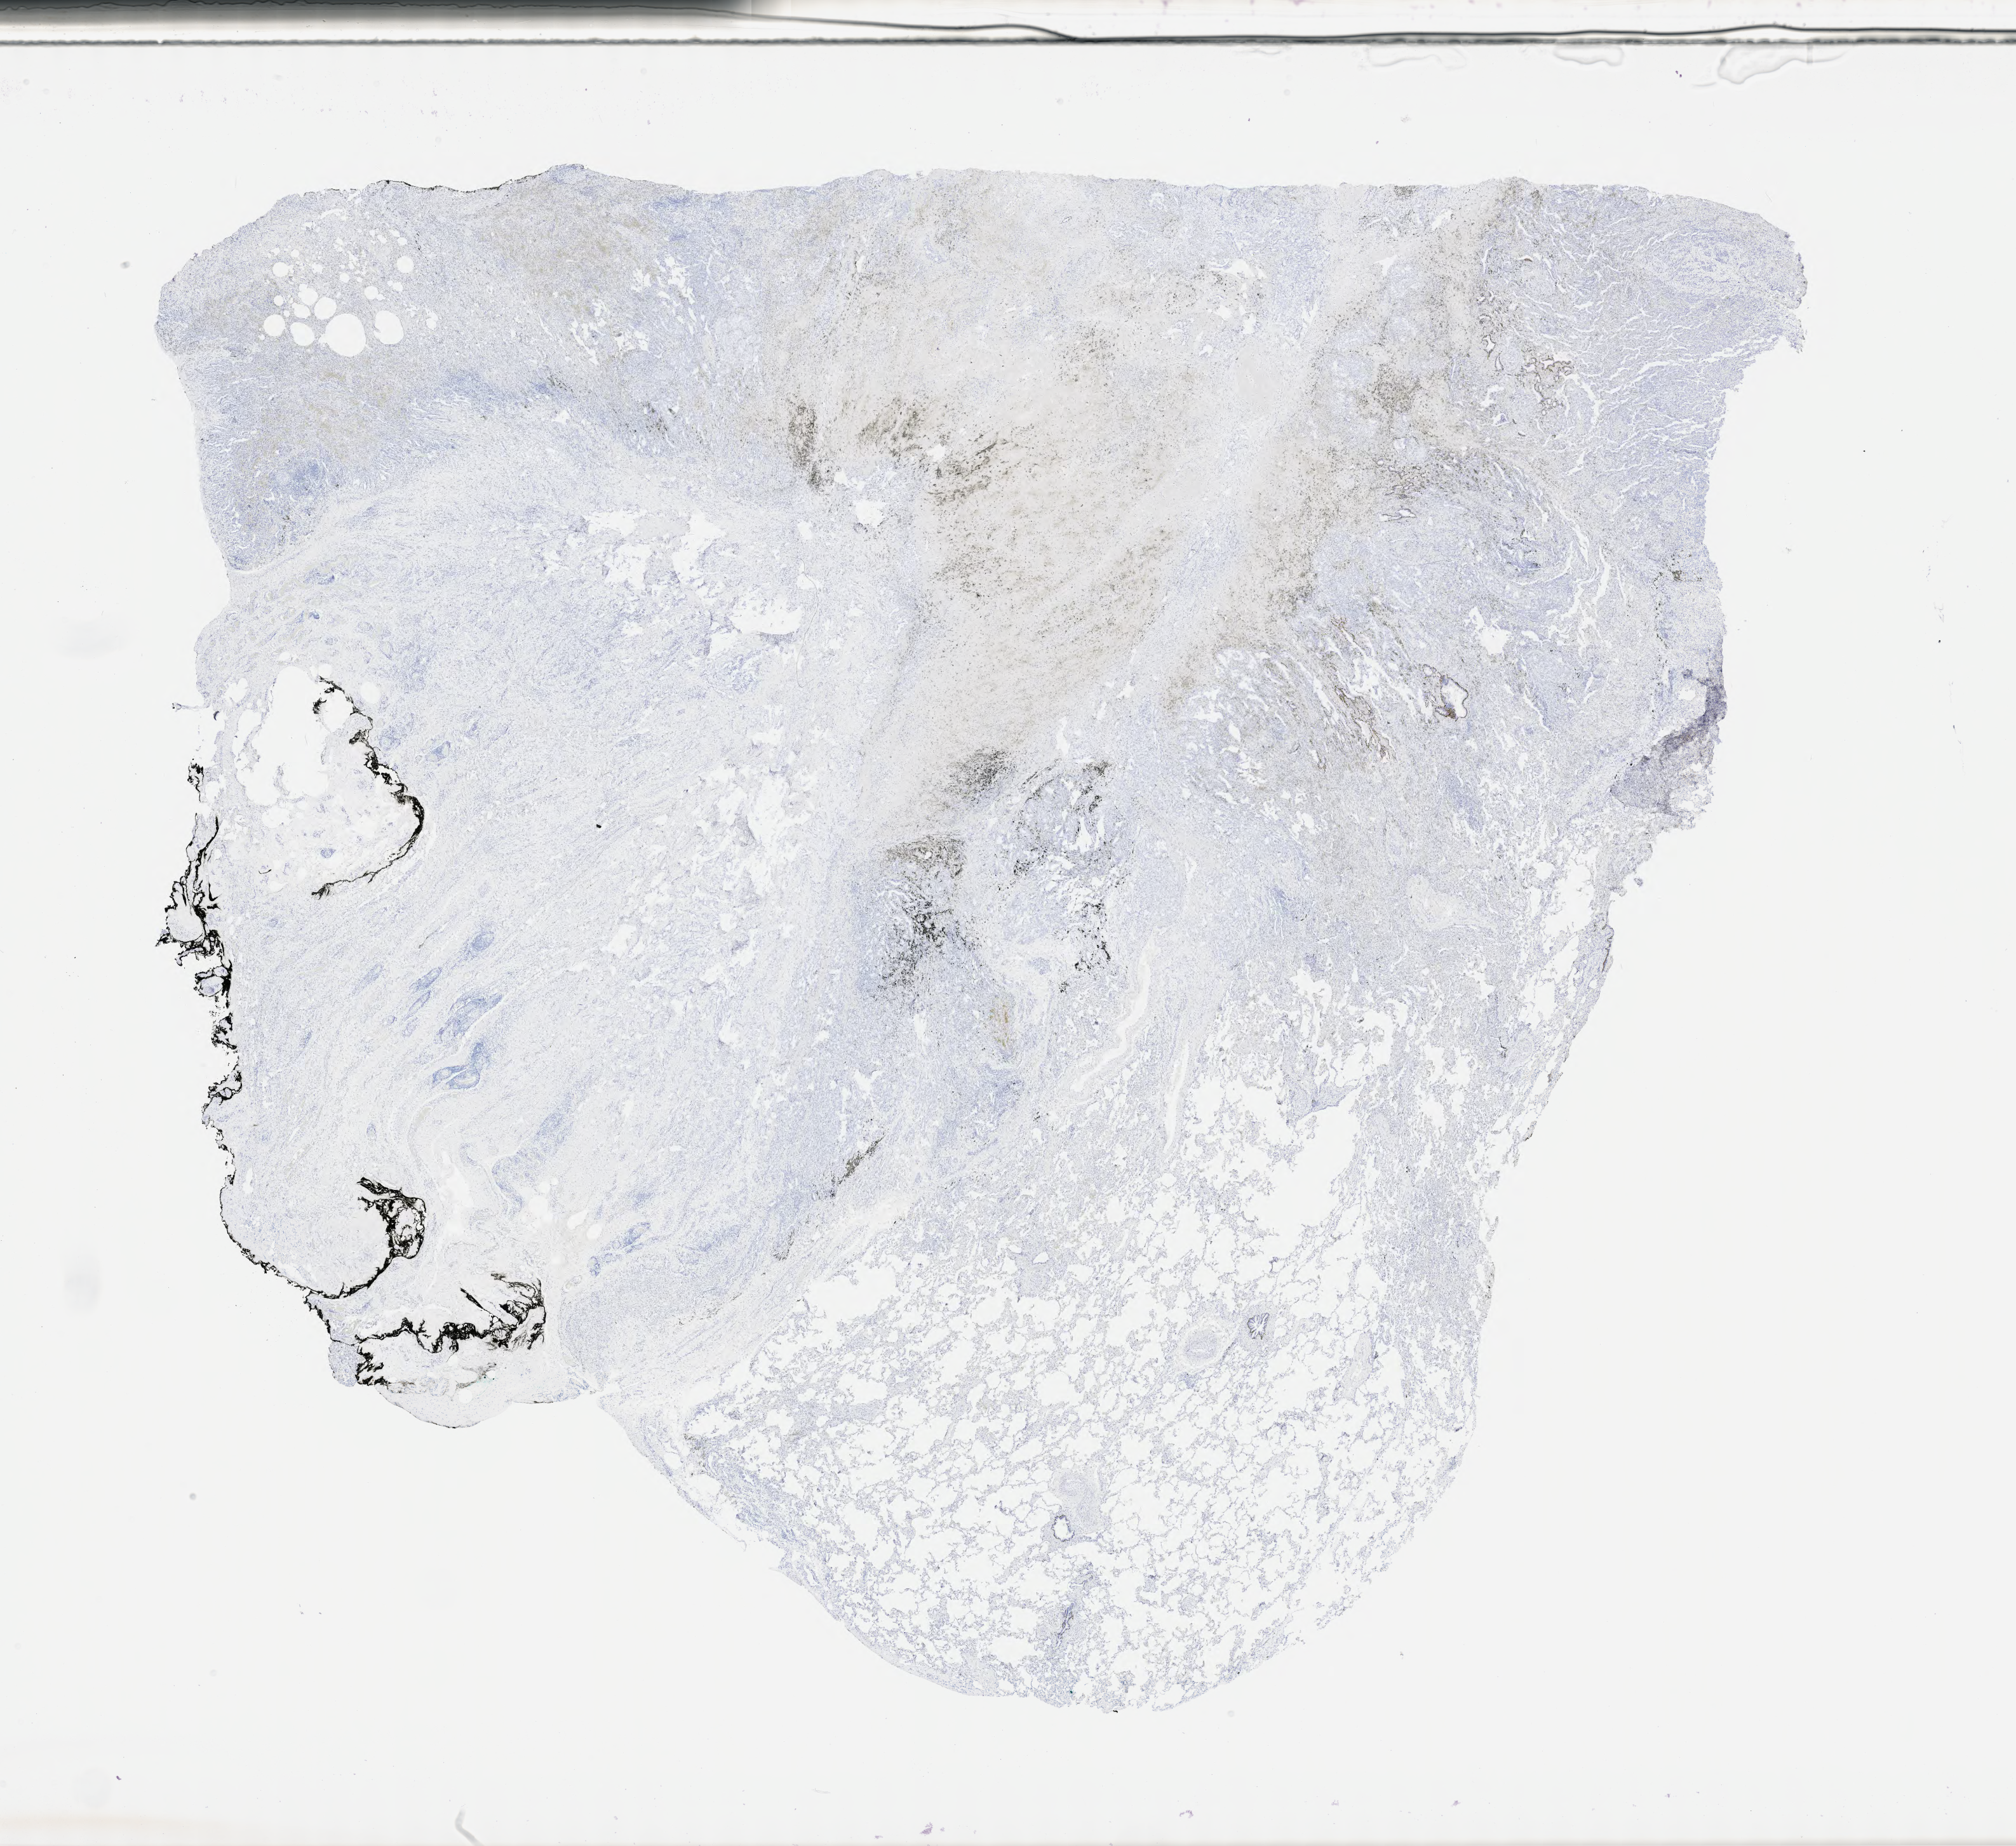
Whole-slide image, immunohistochemical stain for p40 — a low-resolution overview of the entire scanned area, about 25.7 x 23.5 mm, tumor tissue. Patient sex: male.
Diagnosis: Adenocarcinoma, NOS.